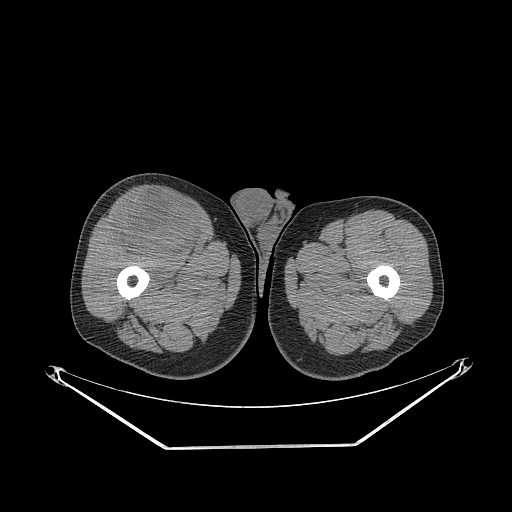
CT of an extremity soft-tissue mass (from a PET/CT study), one axial slice. Position 281 of 311 along the scan axis. Soft-tissue window (W 400 / L 40 HU). 512 × 512 image matrix, field of view 500 × 500 mm. Male patient. Case-level facts recorded for this patient, not image findings: histological type: pleiomorphic leiomyosarcoma; grade: intermediate; site of the primary tumour: right thigh.
Outlined on this slice (expert contour drawn on MRI and transferred to this co-registered scan by the dataset authors):
- gross tumour volume including surrounding oedema: bounding box (x1, y1, x2, y2) in pixels: (112, 192, 202, 259)
- gross tumour volume (mass): (112, 192, 202, 259)